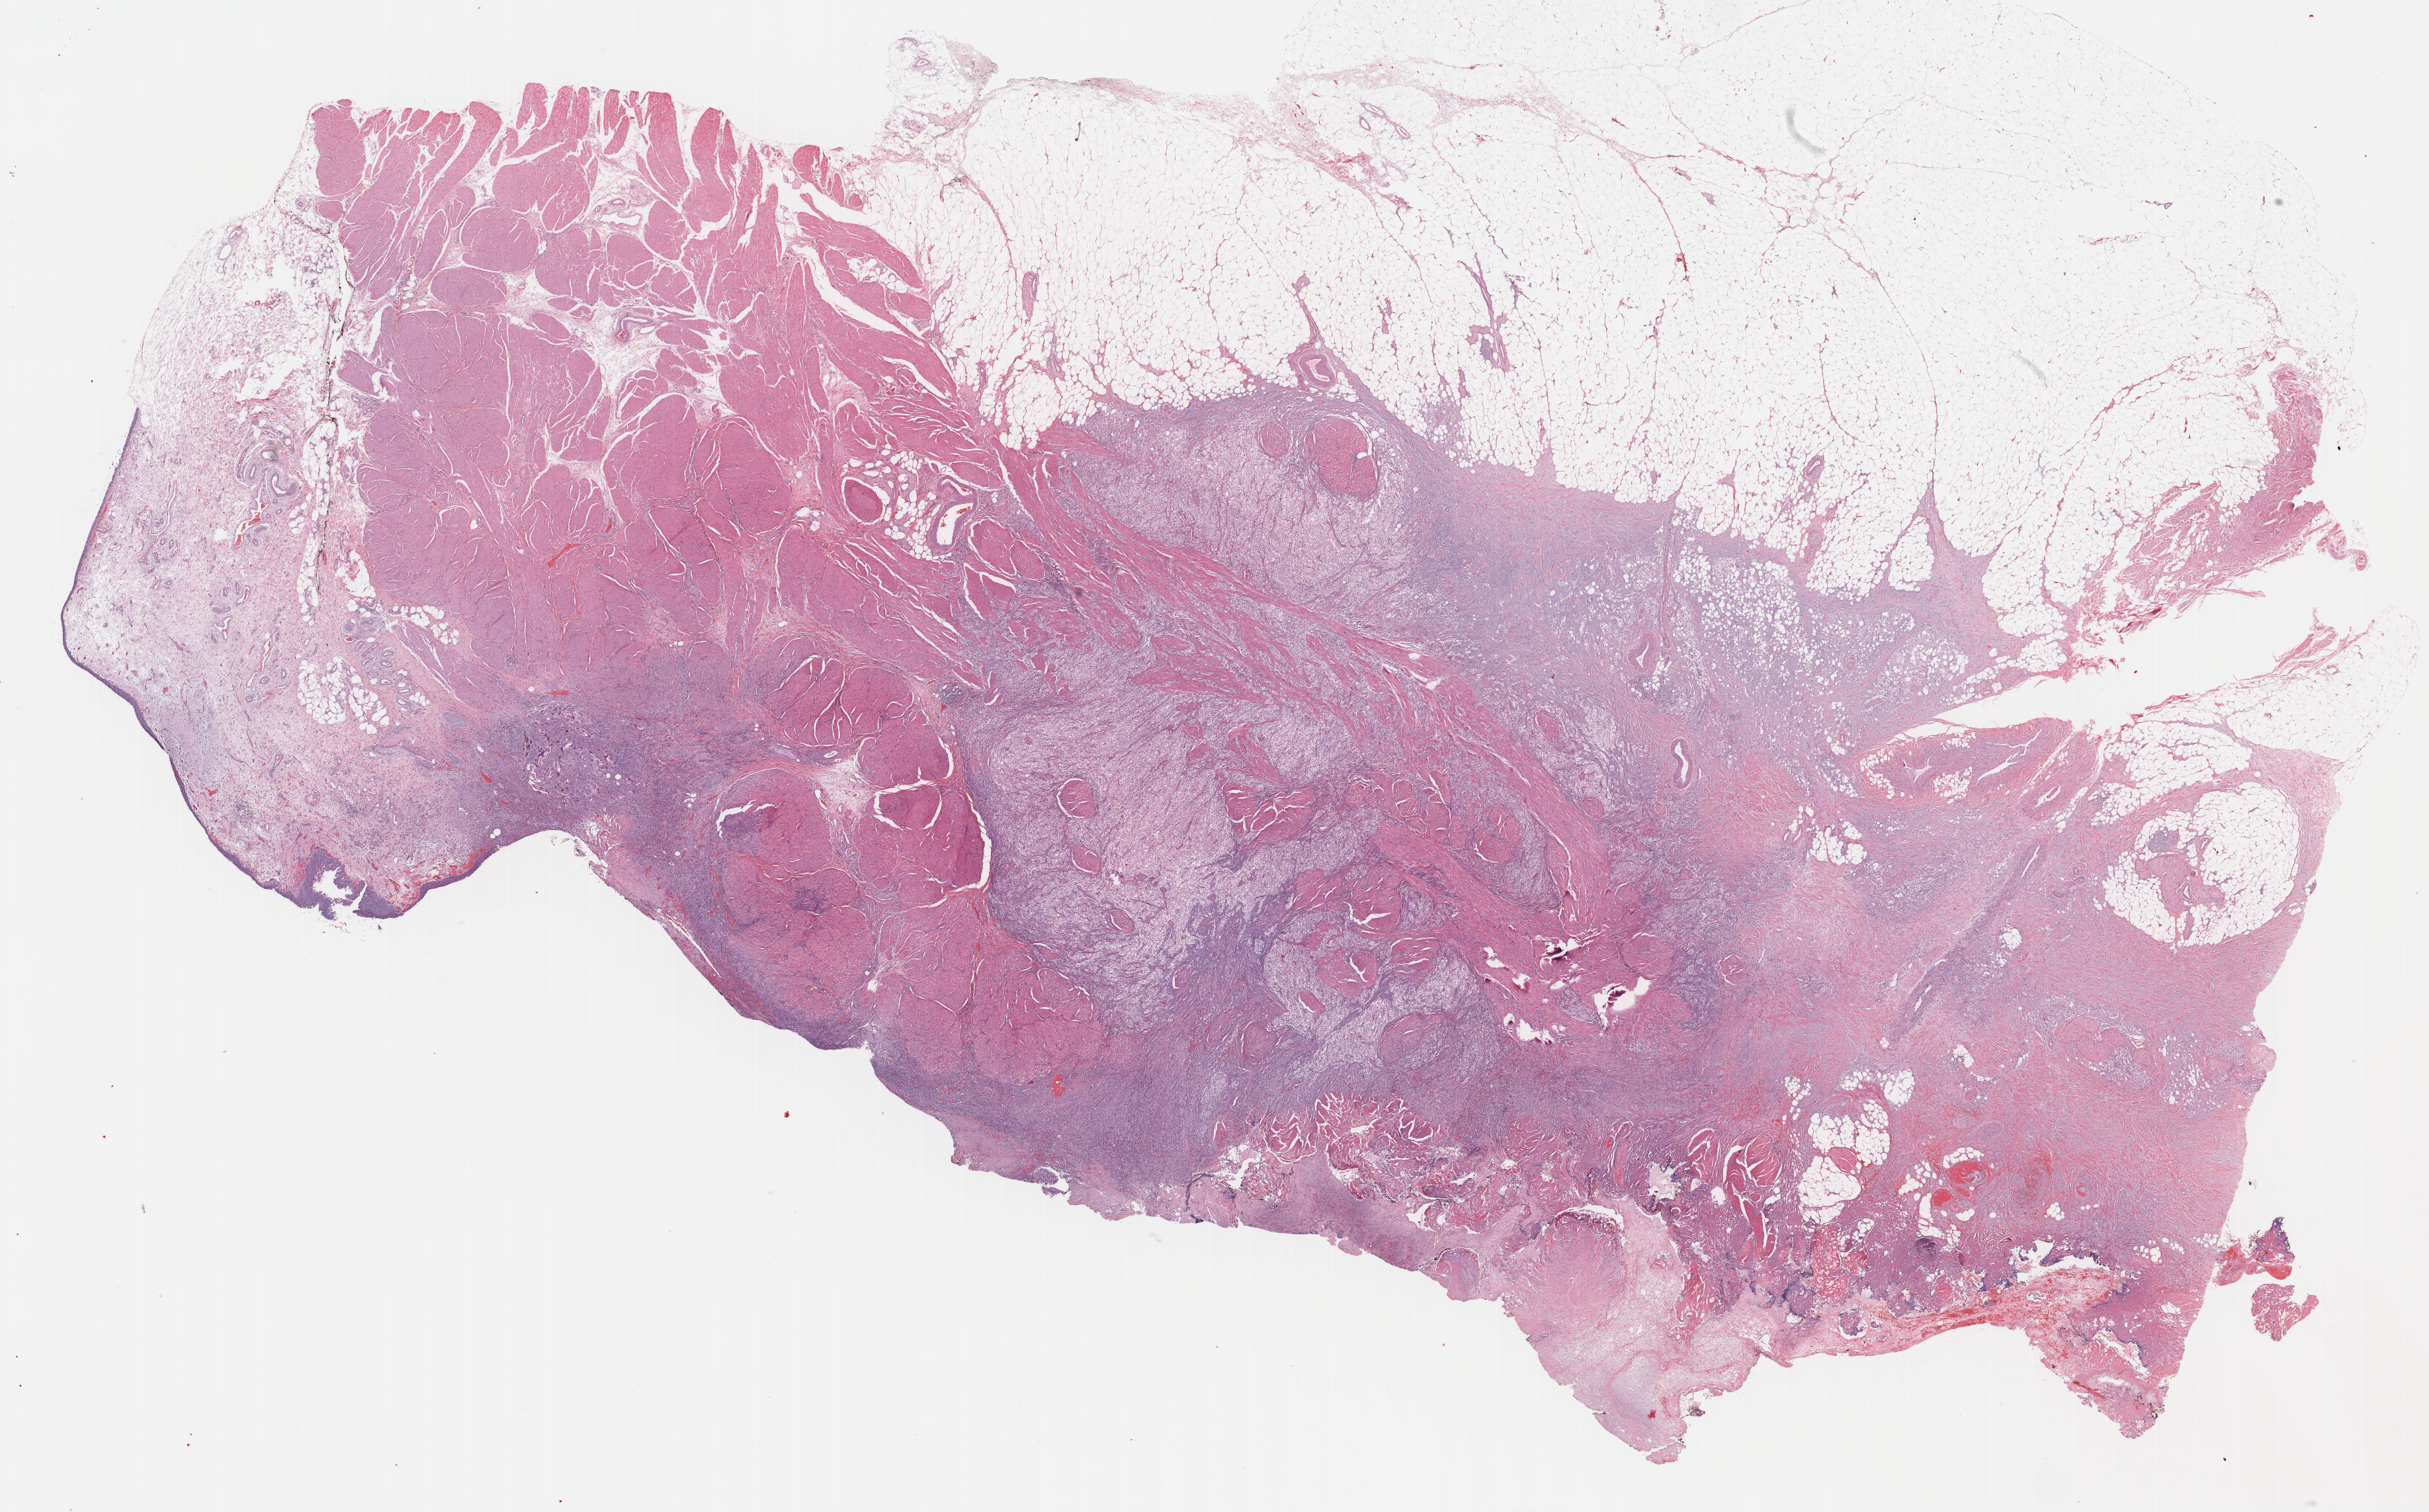
Whole-slide histology image, H&E-stained — shown as a low-resolution overview of the whole scanned area (about 29.7 x 18.5 mm, slide scanned at 40x), FFPE section, primary tumour sample from the bladder. Male patient; age at initial diagnosis 48 years. Histologic grade: high grade.
AJCC pathologic stage: III (6th edition). Pathologic diagnosis: Transitional cell carcinoma.